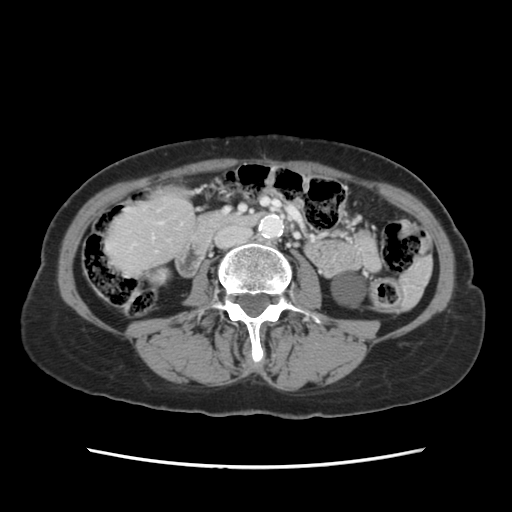
Contrast-enhanced abdominal CT, one axial slice. Slice 19 of 120 in the series (ordered by position). 120 kVp. Soft-tissue window (W 400 / L 40 HU). 2.5 mm slice thickness. 512 × 512 image matrix. Female patient, age 70 years. Case-level facts recorded for this patient, not image findings: diagnosis: colorectal cancer liver metastases, imaged before liver resection; multiple liver metastases: no; largest metastasis: 2.5 cm; disease in both lobes: no.
Structures marked on this image (expert manual segmentation):
- liver: bounding box [x1, y1, x2, y2] px = [109, 192, 191, 271]
- planned liver remnant (the part of the liver to remain after resection): [109, 192, 191, 270]